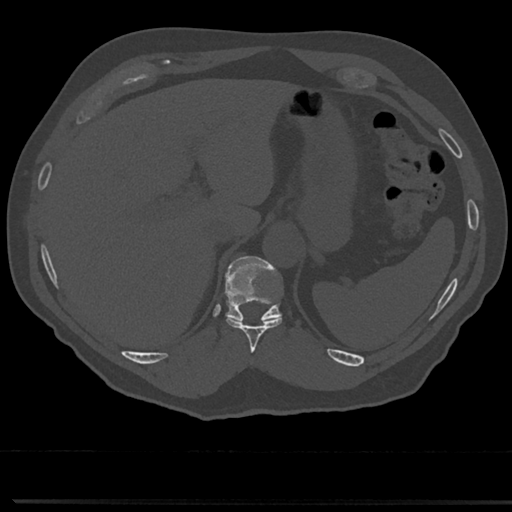
CT including the spine, one axial slice; slice 234 of 817 in the series (ordered by position); reconstruction kernel Br40s/3; 120 kVp; bone window (W 1800 / L 400 HU); 0.5 mm slice thickness; 512 × 512 image matrix, field of view 355 × 355 mm. Male patient, age 61 years. Case-level facts recorded for this patient, not image findings: primary cancer: prostate.
Annotated regions visible in this slice (semi-automatic segmentation, software-assisted and operator-edited):
- T10 vertebra: box from (x=225, y=281) to (x=283, y=350) px
- T11 vertebra: (x=227, y=258)–(x=282, y=322)